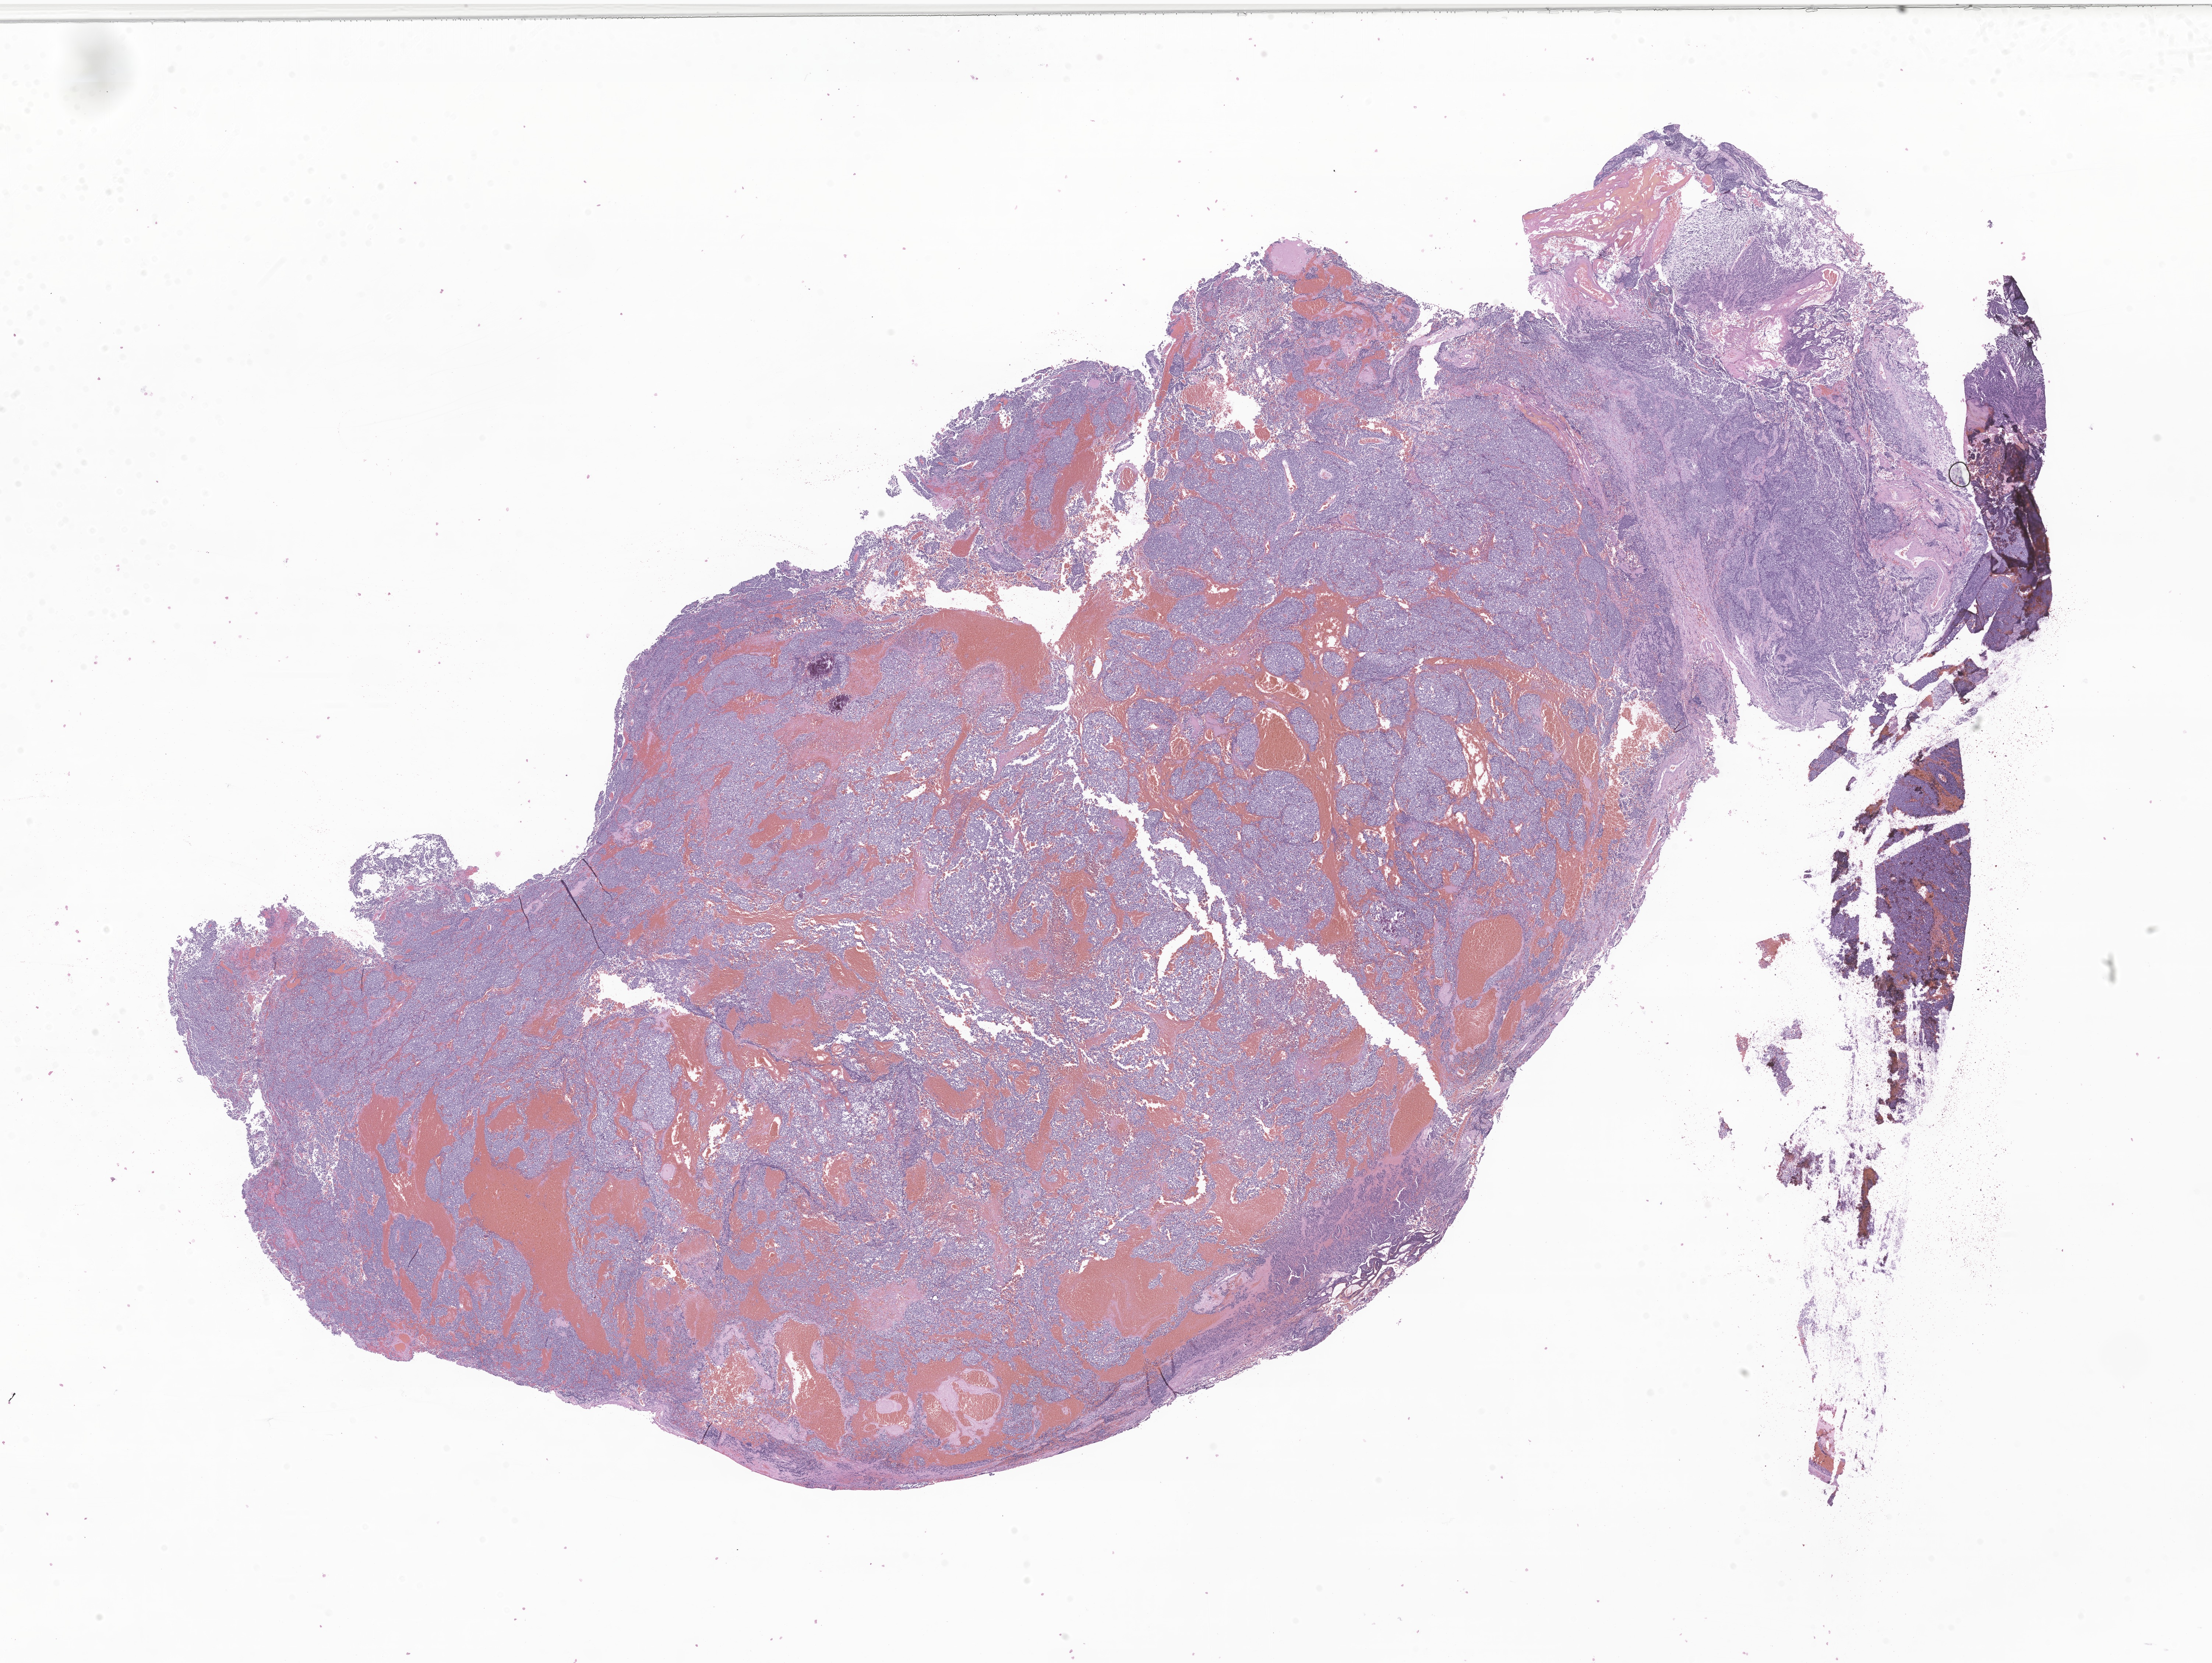
Whole-slide image, haematoxylin and eosin stain of tumor tissue from the pineal gland — shown as a low-resolution overview of the whole scanned area (about 25.3 x 19.0 mm), FFPE section. Female patient, age 38 months (3 years 2 months).
Diagnosis (ICD-O-3 morphology term): Pineoblastoma.